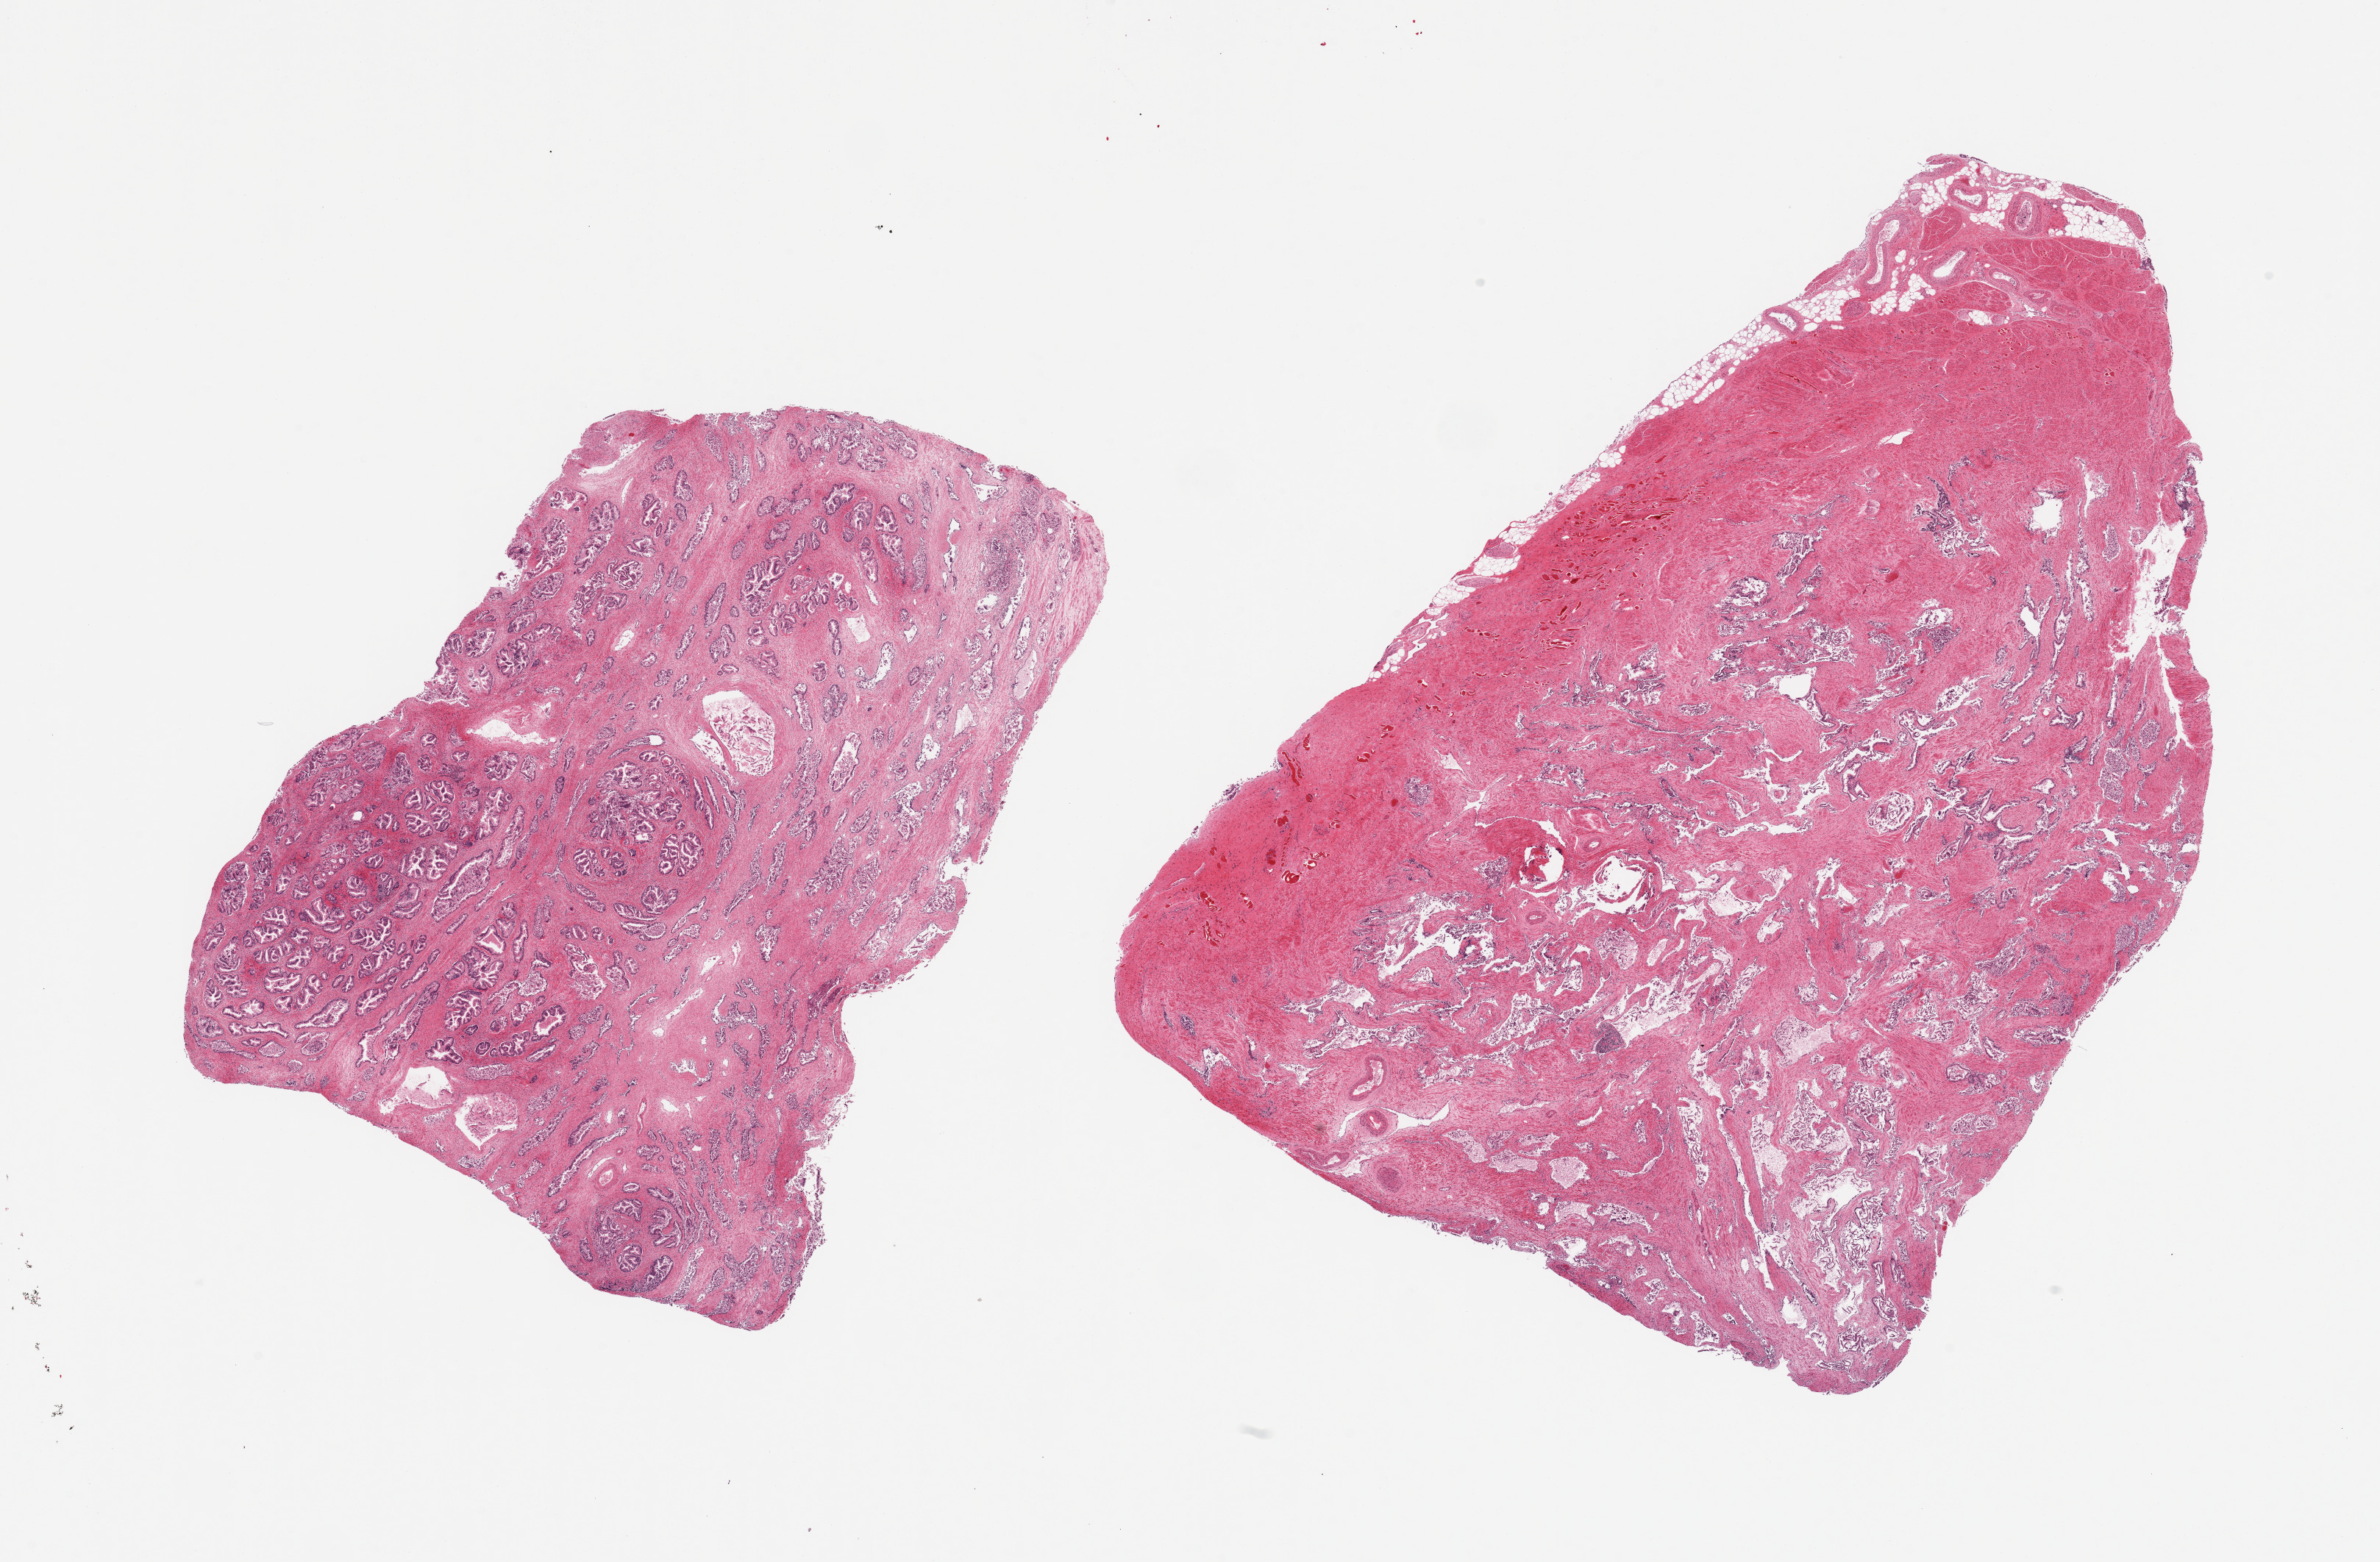
Whole-slide image, H&E stain — whole scanned area (about 25.6 x 16.8 mm, slide scanned at 20x) shown as a low-resolution overview; PAXgene-fixed, paraffin-embedded tissue; sampled site (target tissue): prostate; donor tissue sample. Male donor.
Pathologist's review note for this sample: 2 pieces. nodular hyperplastic glandular pattern.